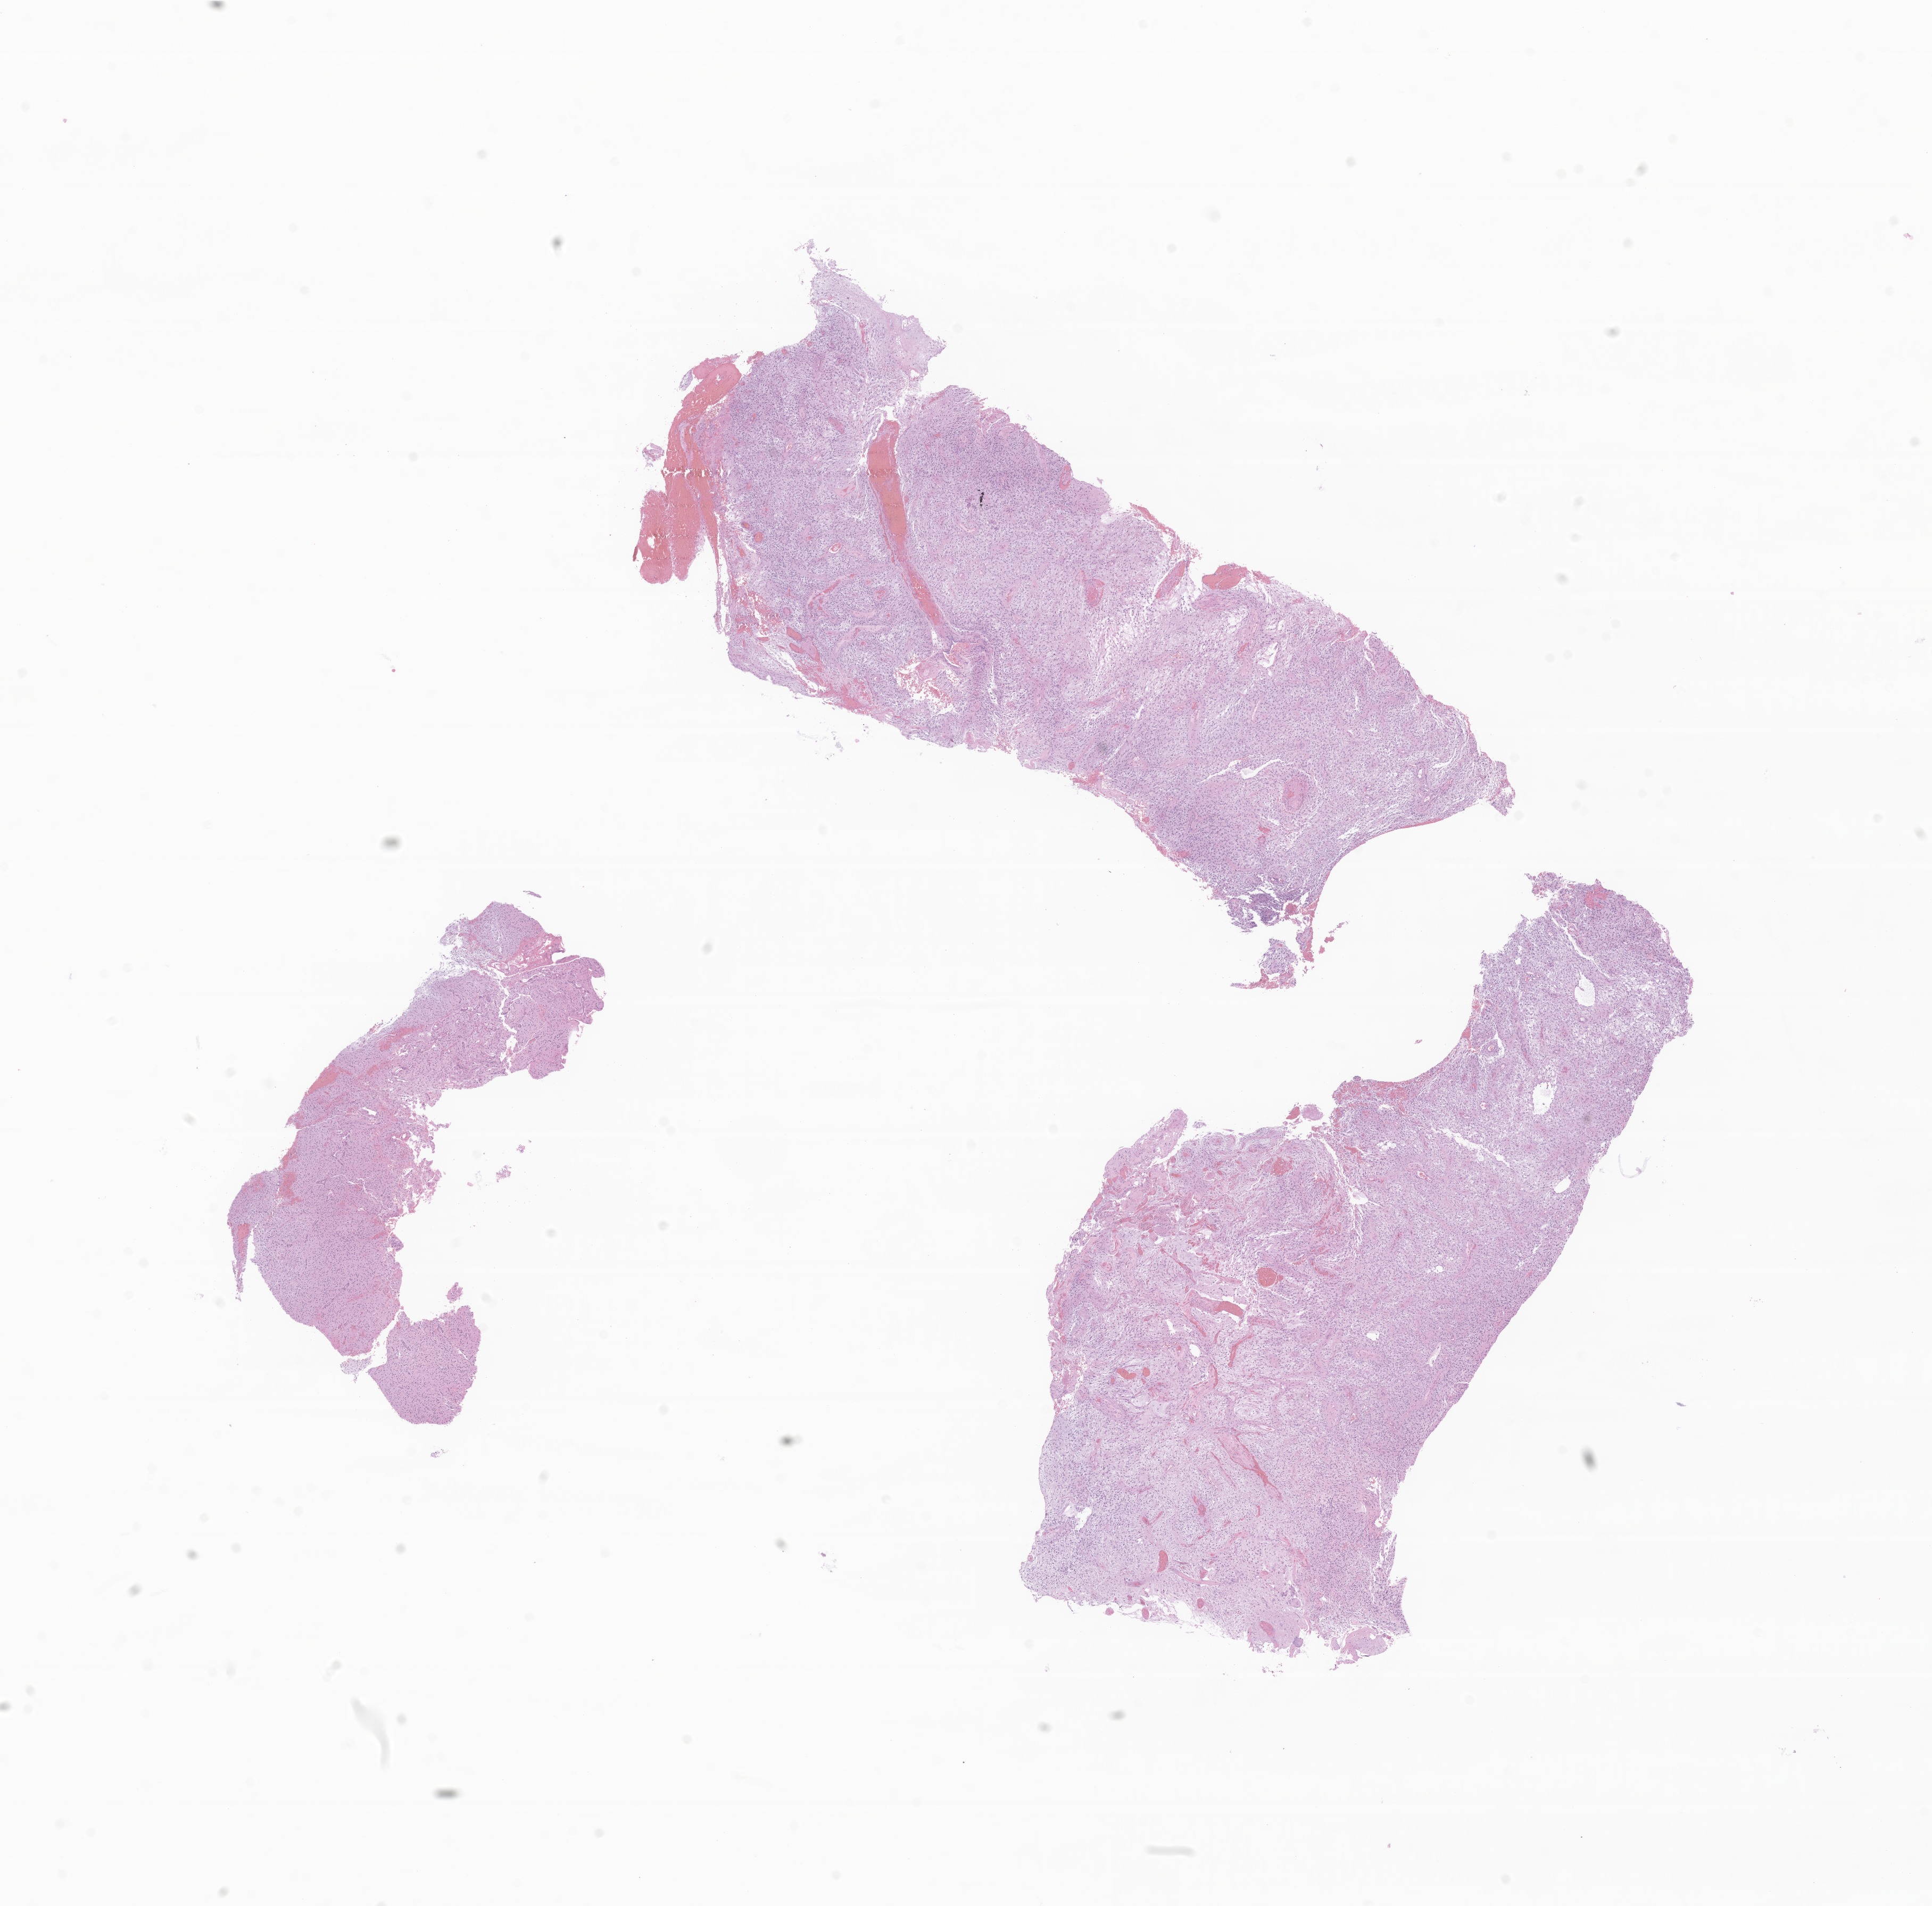
Whole-slide image, H&E stain of tumor tissue from the brain — shown as a low-resolution overview of the whole scanned area (about 15.3 x 15.1 mm); FFPE section. Patient: female, age 88 months (7 years 4 months).
Diagnosis: Neoplasm, uncertain whether benign or malignant.